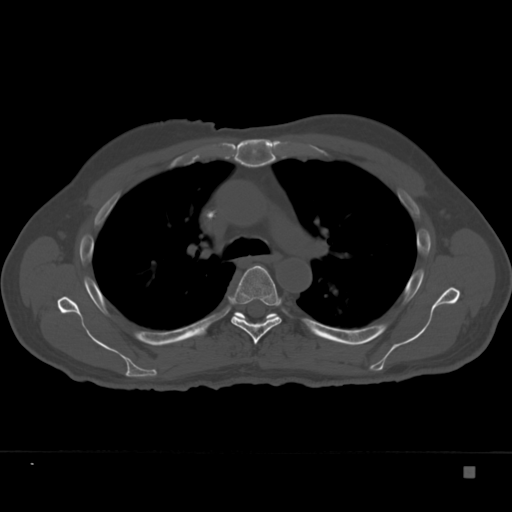
CT including the spine, one axial slice; position 254 of 332 along the scan axis; reconstruction kernel Br40s; 120 kVp; bone window (W 1800 / L 400 HU); 512 × 512 image matrix, field of view 389 × 389 mm. Male patient, age 72 years. Case-level facts recorded for this patient, not image findings: primary cancer: skeletal.
Annotated regions visible in this slice (semi-automatic segmentation, software-assisted and operator-edited):
- T5 vertebra: bounding box [x1, y1, x2, y2] px = [228, 265, 282, 344]
- T6 vertebra: [233, 311, 278, 321]